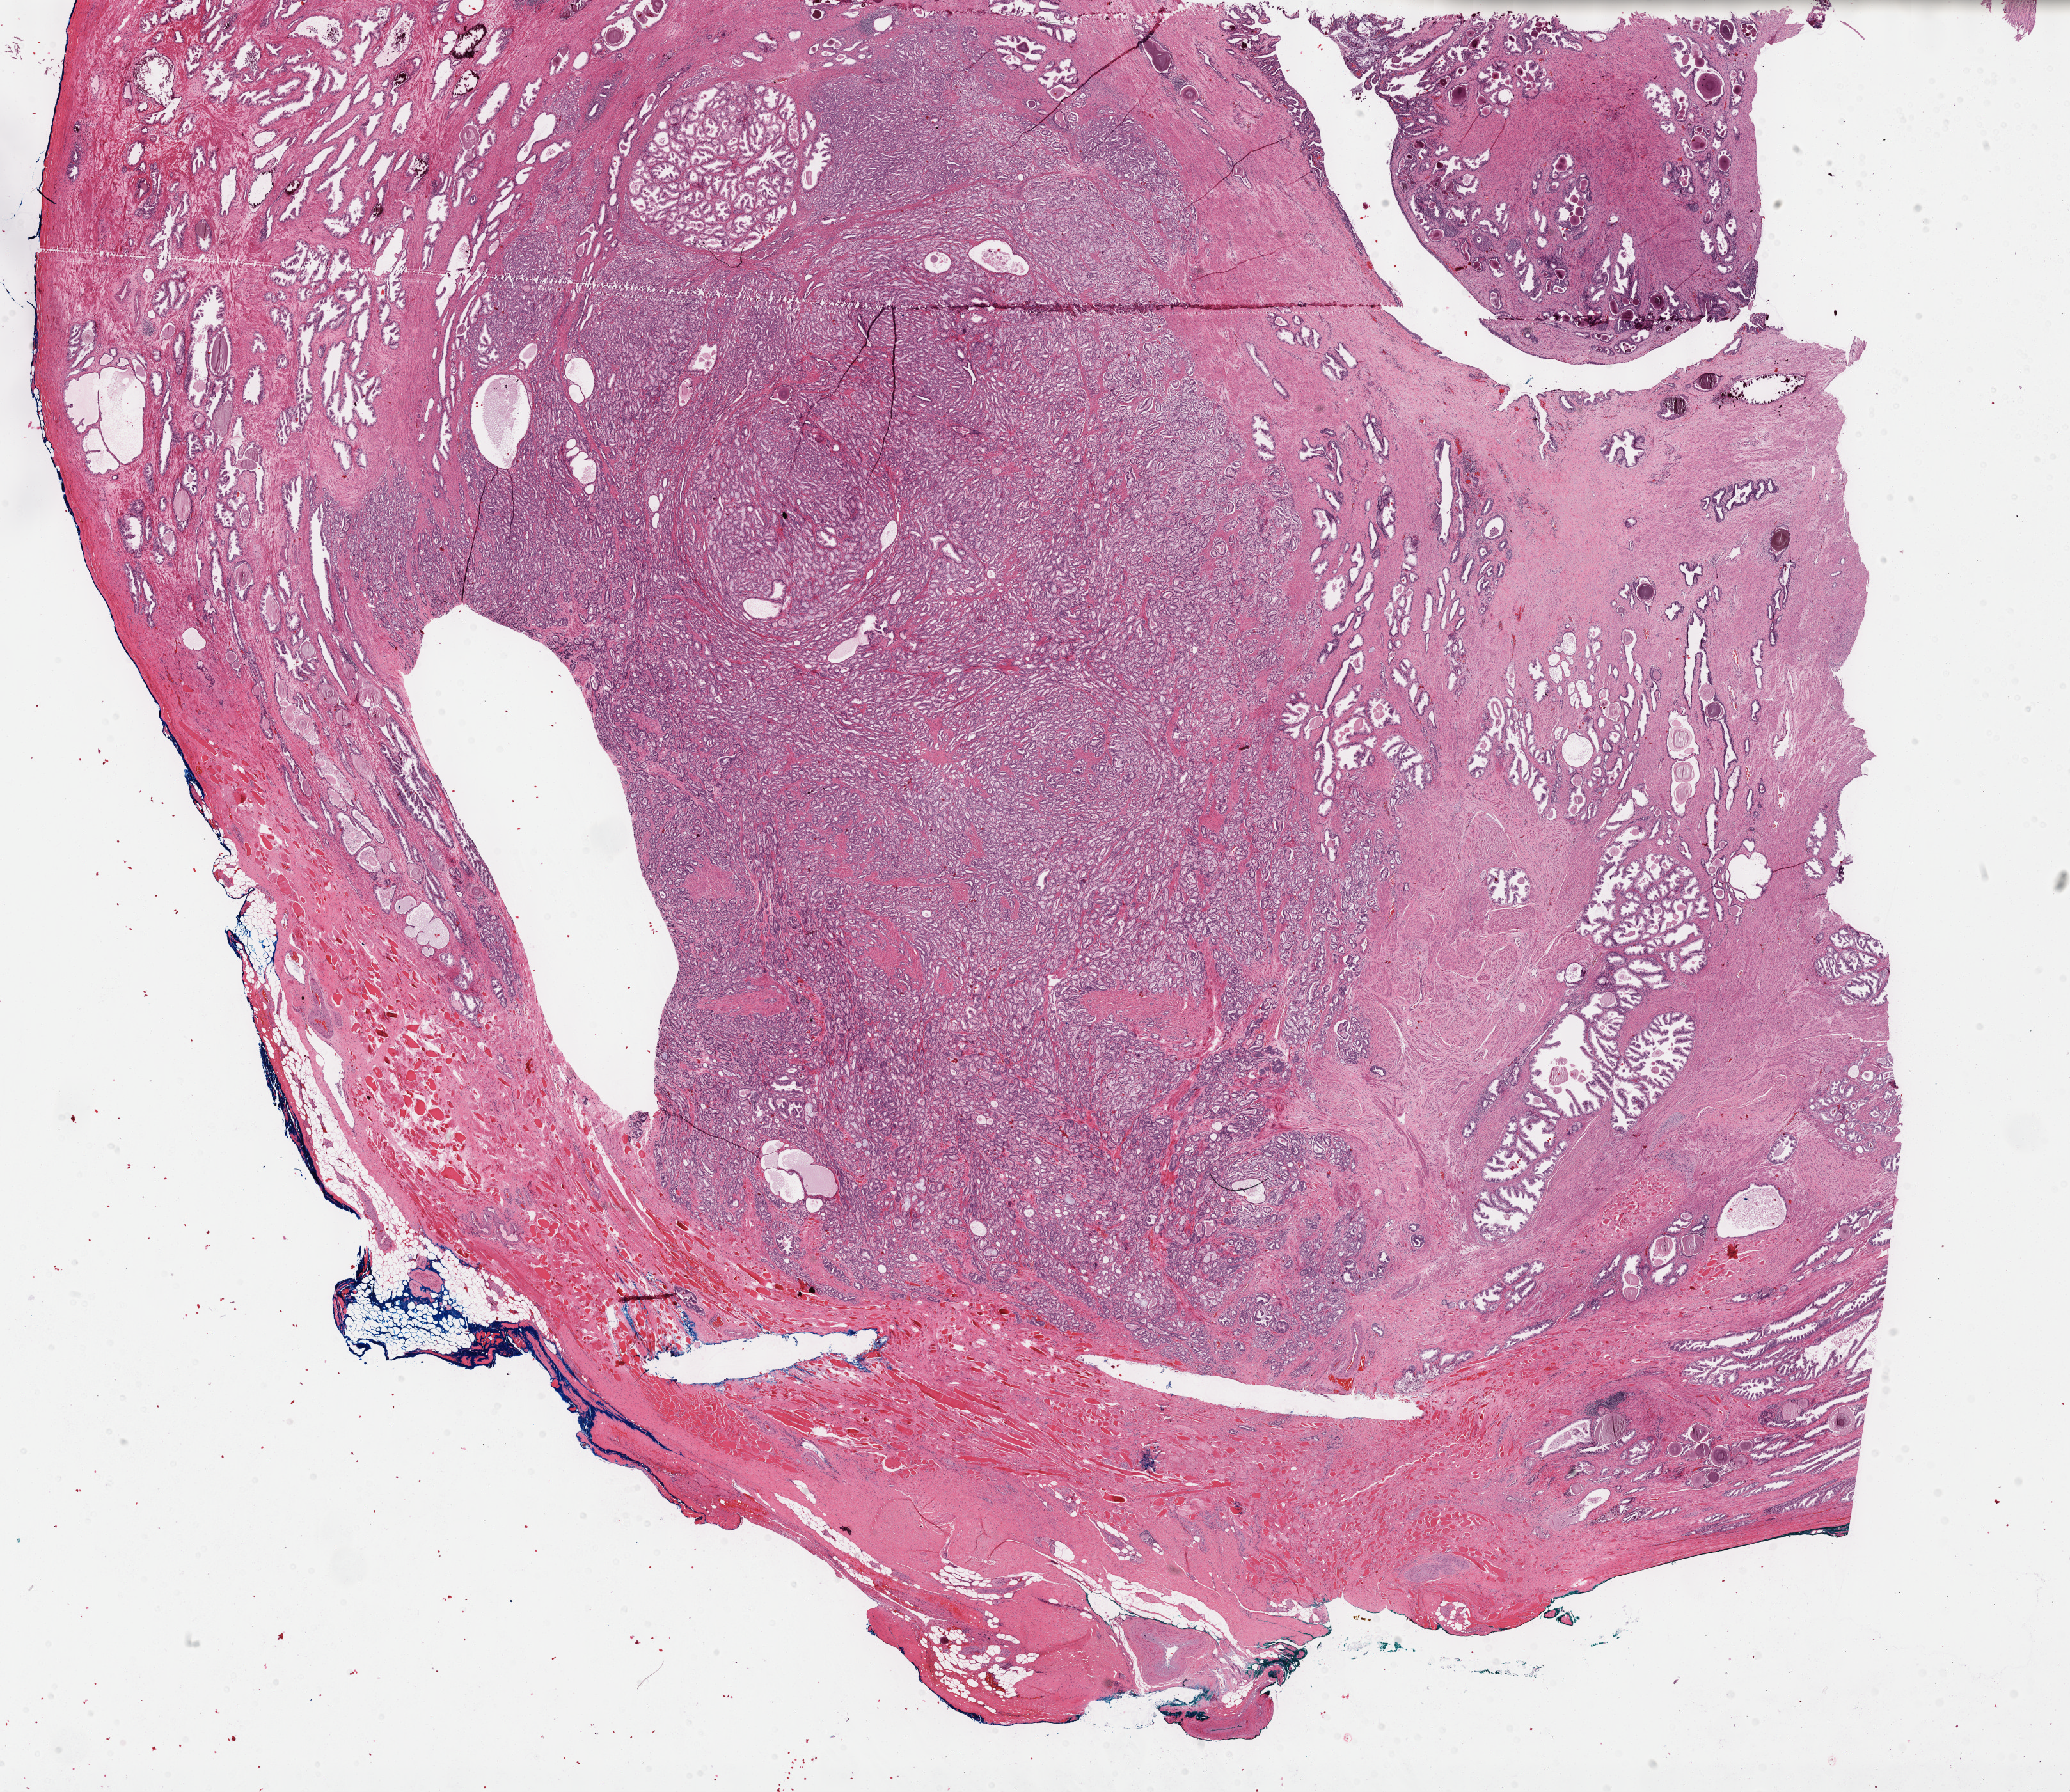
Whole-slide histology image, H&E-stained, low-resolution overview of the scanned area, about 26.2 x 22.7 mm. Formalin-fixed paraffin-embedded (FFPE) diagnostic section. Sample: primary tumour, prostate. Patient: male, age at initial diagnosis 56 years. Gleason score: 6 (3+3).
Pathologic diagnosis: Adenocarcinoma, NOS (prostate gland). Lymph nodes positive (case pathology): 0 of 28 examined.